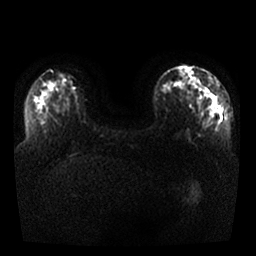
Breast MRI, one axial slice. Position 9 of 25 along the scan axis. Diffusion-weighted series; image 2 of 4 stored at this slice position (different b-values; order by instance number). 1.5 T. 4 mm slice thickness. 256 × 256 image matrix. Female patient.
Annotated regions visible in this slice (manually delineated by an expert):
- tumour on diffusion-weighted imaging: bounding box [x1, y1, x2, y2] px = [179, 68, 204, 88]